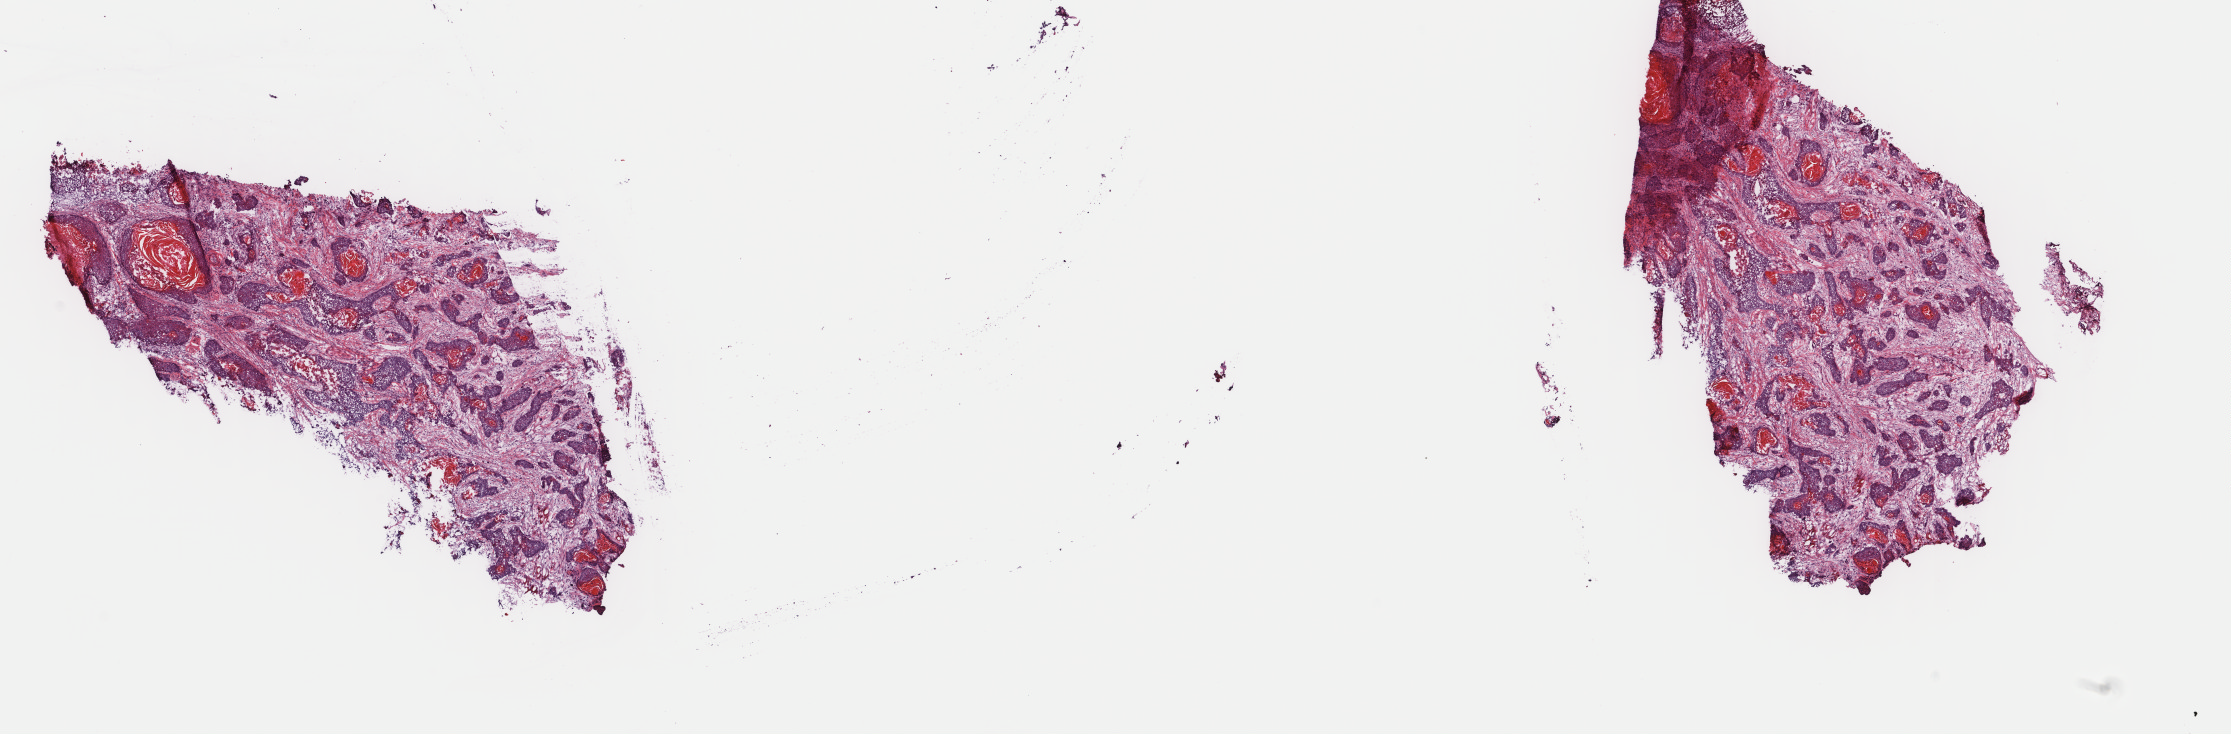
Digitized H&E-stained tissue section (whole slide), whole scanned area (about 17.7 x 5.8 mm, acquisition: 40x scan) shown as a low-resolution overview. Frozen section from the top of the tissue portion. Head and neck, primary tumour sample. Male, age 67 years at initial diagnosis. Histologic grade: G1 (well differentiated). Pathologist review of this section (percent, as recorded): tumour cells 50%, tumour nuclei 60%, normal cells 0%, stromal cells 50%, necrosis 0%. Infiltration values recorded for this section: lymphocyte infiltration 0%, monocyte infiltration 0%, neutrophil infiltration 0%.
Diagnosis: Squamous cell carcinoma, NOS (floor of mouth, NOS). AJCC pathologic stage: IVA (7th edition).